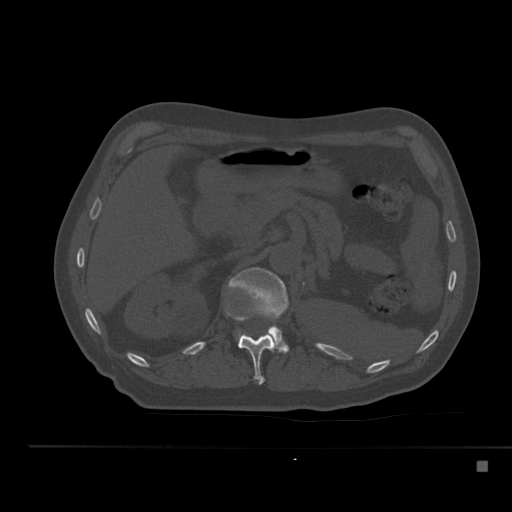
CT including the spine, one axial slice; slice 221 of 517 in the series (ordered by position); reconstruction kernel Br40s; 120 kVp; bone window (W 1800 / L 400 HU); 1.5 mm slice thickness; 512 × 512 image matrix. Patient: male, 70 years. Case-level facts recorded for this patient, not image findings: primary cancer: renal; vertebrae with lytic lesions (as recorded): T4, T6, T10, T12, L3, L4, L5.
Annotated regions visible in this slice (semi-automatically segmented with operator editing):
- L1 vertebra: bounding box [x1, y1, x2, y2] px = [227, 267, 289, 353]
- T12 vertebra: [225, 309, 276, 385]